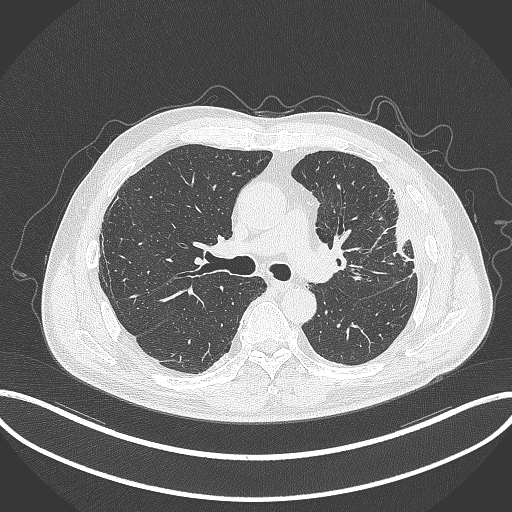
Chest CT, one axial slice. Position 210 of 382 along the scan axis. Reconstruction kernel B70f. 120 kVp. Lung window (W 1500 / L -600 HU). 1 mm slice thickness. 512 × 512 image matrix, field of view 415 × 415 mm. Male patient, age 64 years. Case-level facts recorded for this patient, not image findings: clinical TNM (as recorded): T4 N1 M0; histopathological grade: G3.
Outlined on this slice (rectangle marked by the reading radiologist):
- lung tumour (recorded histology: adenocarcinoma): bounding box <385,211,415,265> (left, top, right, bottom; pixels)